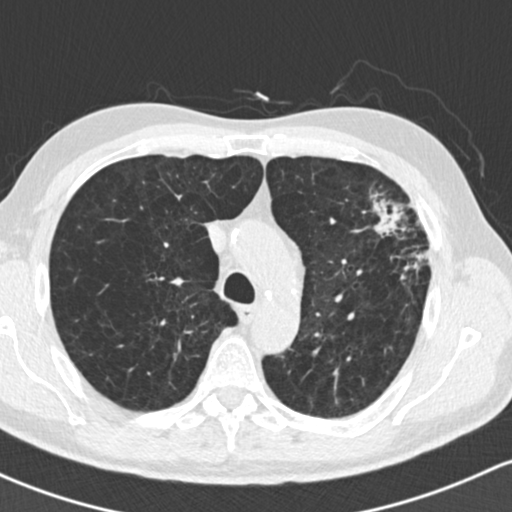
Low-dose screening chest CT, one axial slice; slice 113 of 162 in the series (ordered by position); reconstruction kernel B30f; 120 kVp; lung window (W 1500 / L -600 HU); 2 mm slice thickness; 512 × 512 image matrix, field of view 318 × 318 mm.
Annotated regions visible in this slice (manually delineated by an expert):
- lesion 1 (tumor, upper lobe of left lung): bounding box [x1, y1, x2, y2] px = [373, 199, 418, 255]